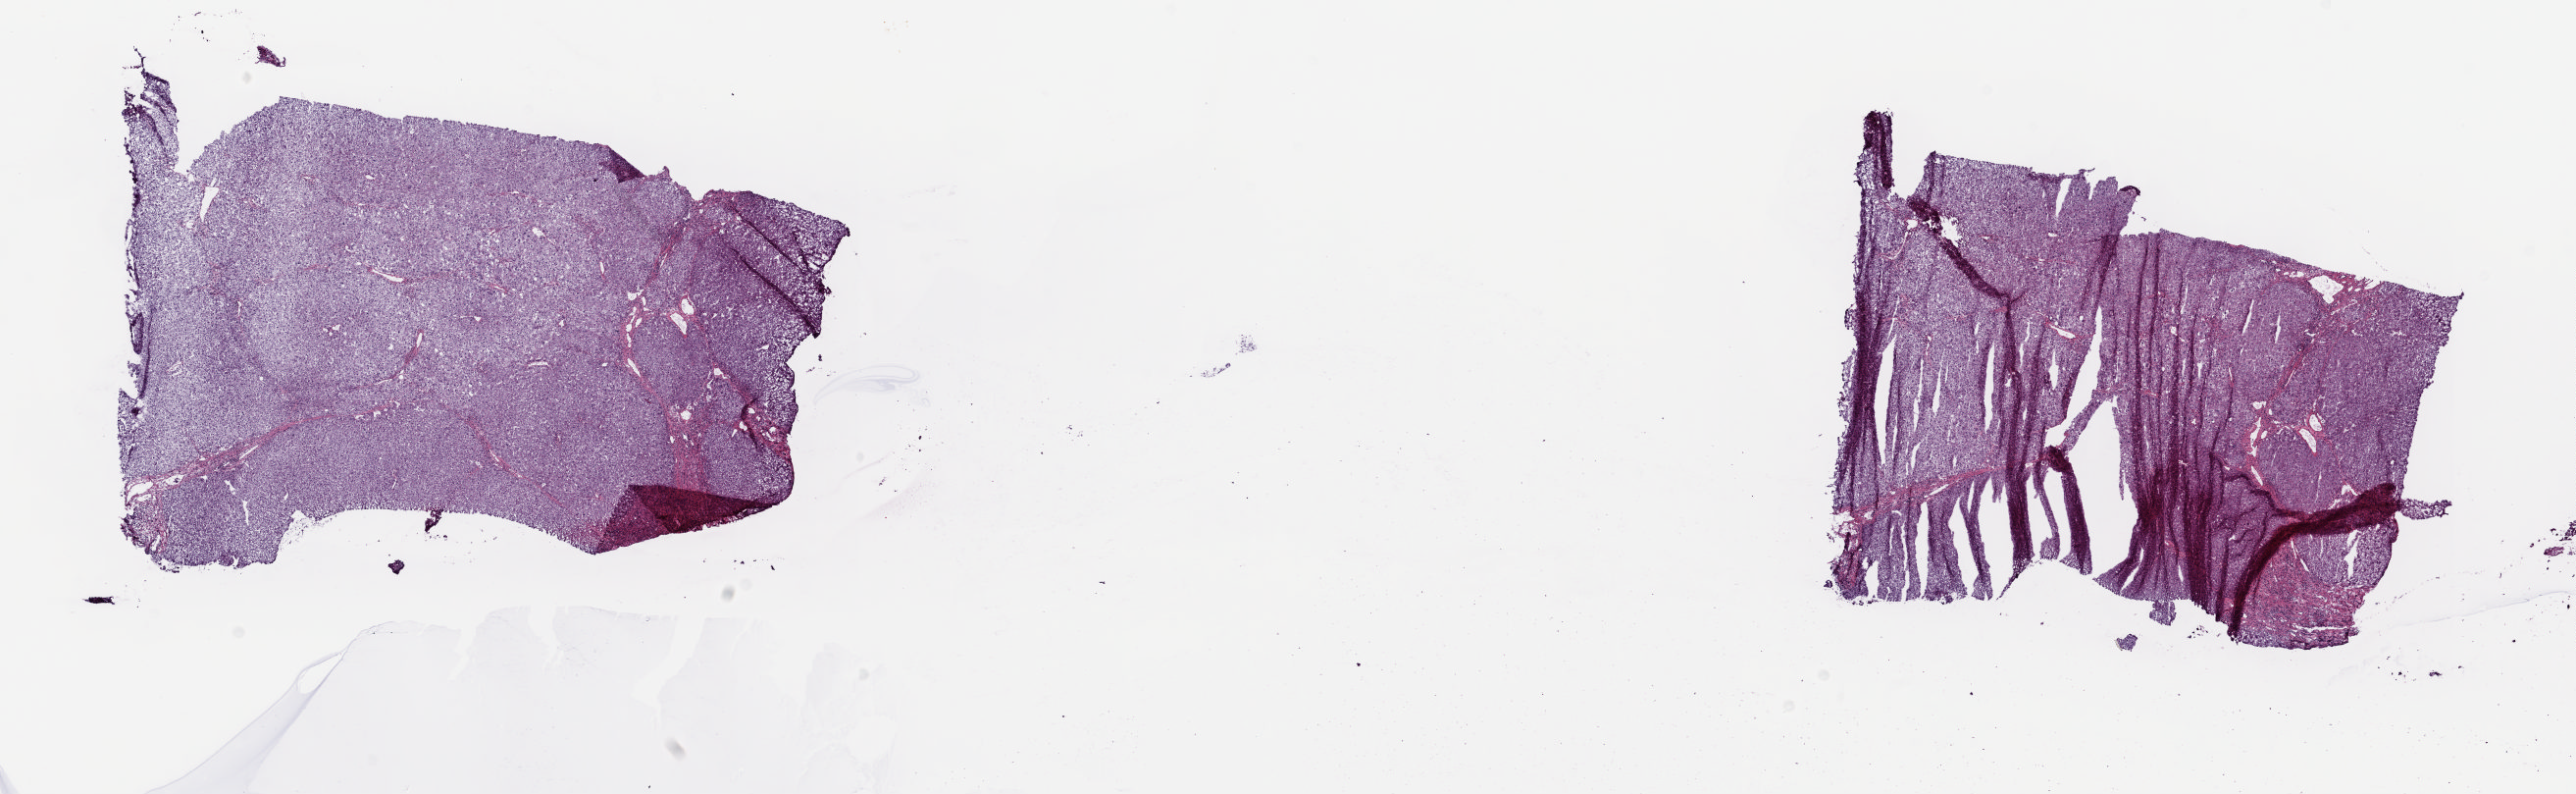
Whole-slide histology image, H&E-stained — shown as a low-resolution overview of the whole scanned area (about 20.8 x 6.4 mm). Frozen section from the top of the tissue portion. Liver, solid tissue normal (non-tumour tissue) sample. Patient: male, age at initial diagnosis 23 years. Composition of this section per pathologist review: tumour cells 0%, tumour nuclei 0%, normal cells 90%, stromal cells 10%, necrosis 0%. Inflammatory infiltration, as recorded: lymphocyte infiltration 3%, monocyte infiltration 0%, neutrophil infiltration 0%.
* this section: solid tissue normal (non-tumour) sample from the same patient
* patient diagnosis: Hepatocellular carcinoma, NOS